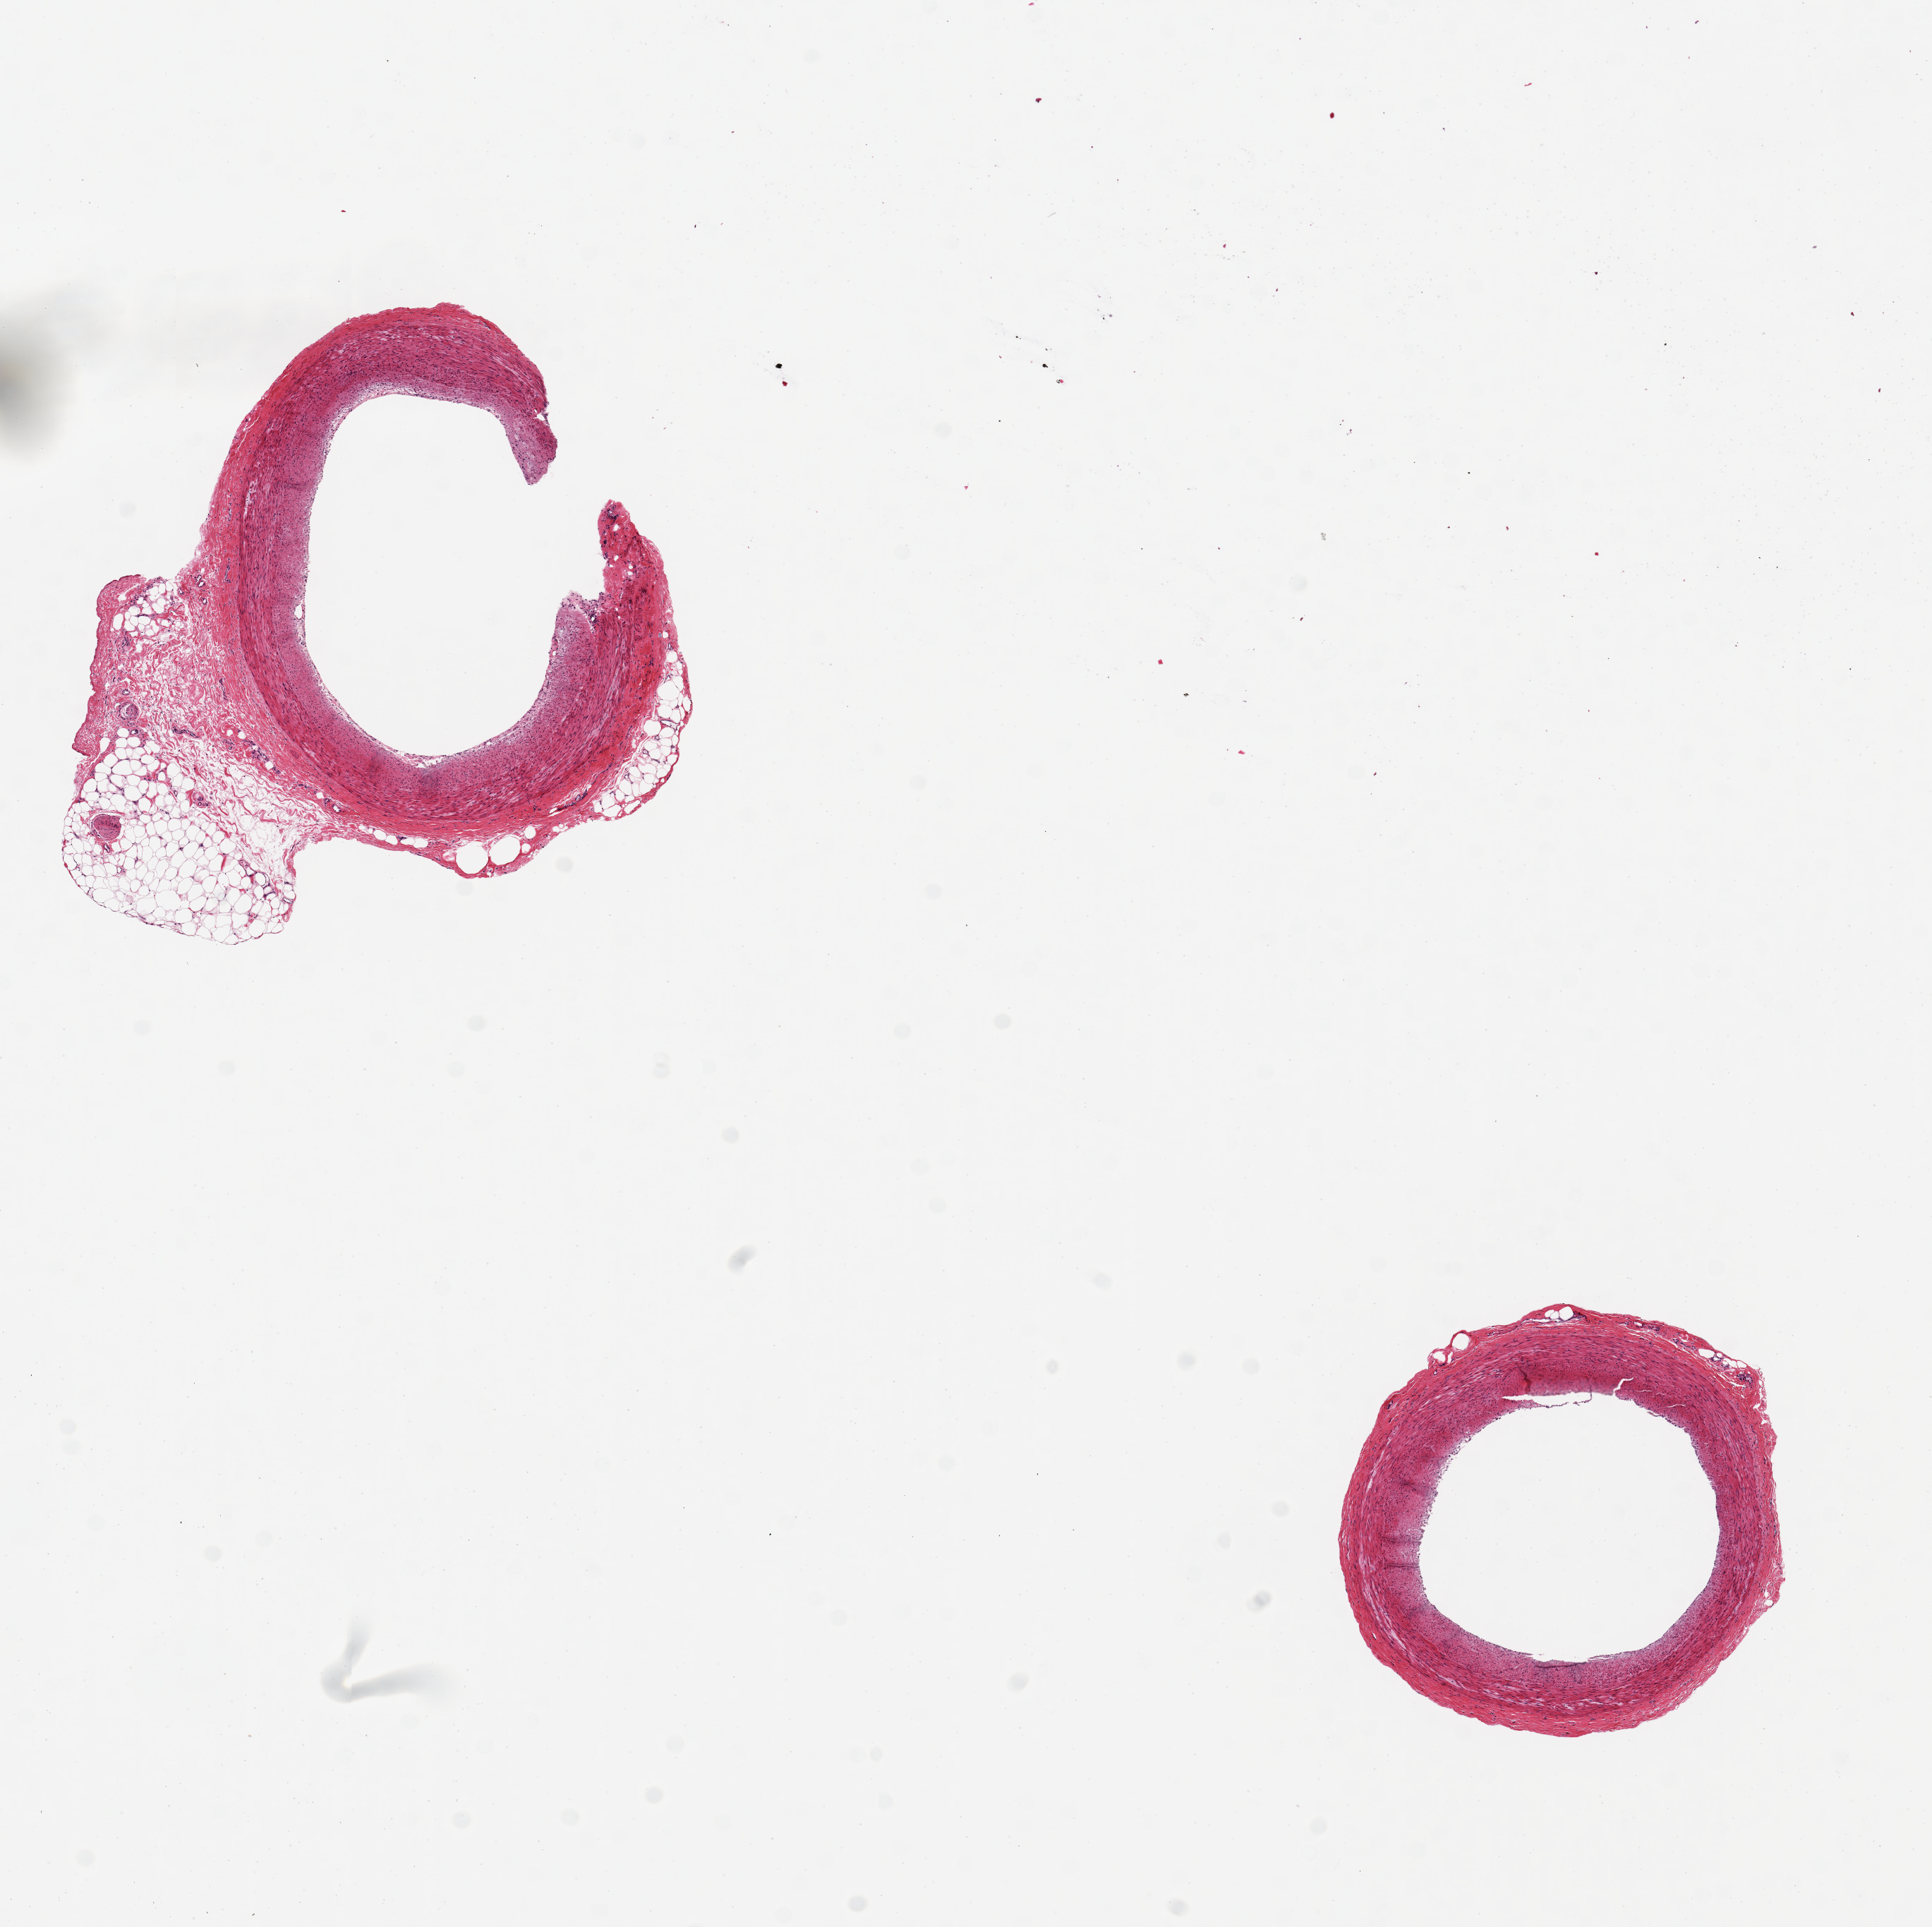
Haematoxylin and eosin whole-slide image, brightfield, whole scanned area (about 10.8 x 10.8 mm) shown as a low-resolution overview. PAXgene-fixed paraffin-embedded (PFPE) section. Sampled site (target tissue): coronary artery. Donor tissue sample. Donor: male.
Reviewer comment on this tissue sample: 2 pieces ~2.5mm d. Minimal atherosis, one has nubbin of adherent fat ~1mm d.